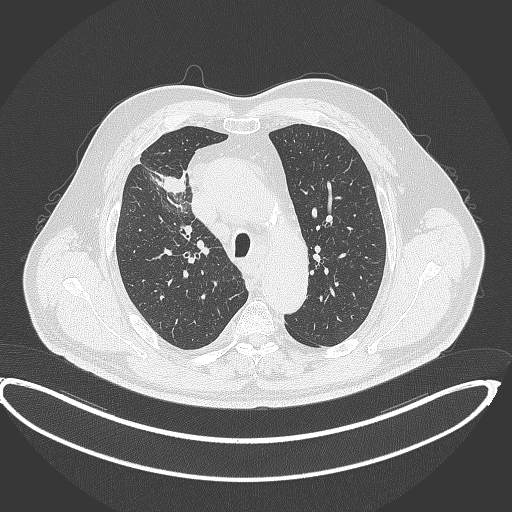
Chest CT, one axial slice. Position 298 of 390 along the scan axis. Reconstruction kernel B70f. 120 kVp. Lung window (W 1500 / L -600 HU). 1 mm slice thickness. 512 × 512 image matrix, field of view 448 × 448 mm. Male patient, age 62 years. Case-level facts recorded for this patient, not image findings: clinical TNM (as recorded): T1c N3 M1c.
Structures marked on this image (bounding box drawn by a radiologist):
- lung tumour (recorded histology: adenocarcinoma): bounding box (x1, y1, x2, y2) in pixels: (158, 174, 187, 196)